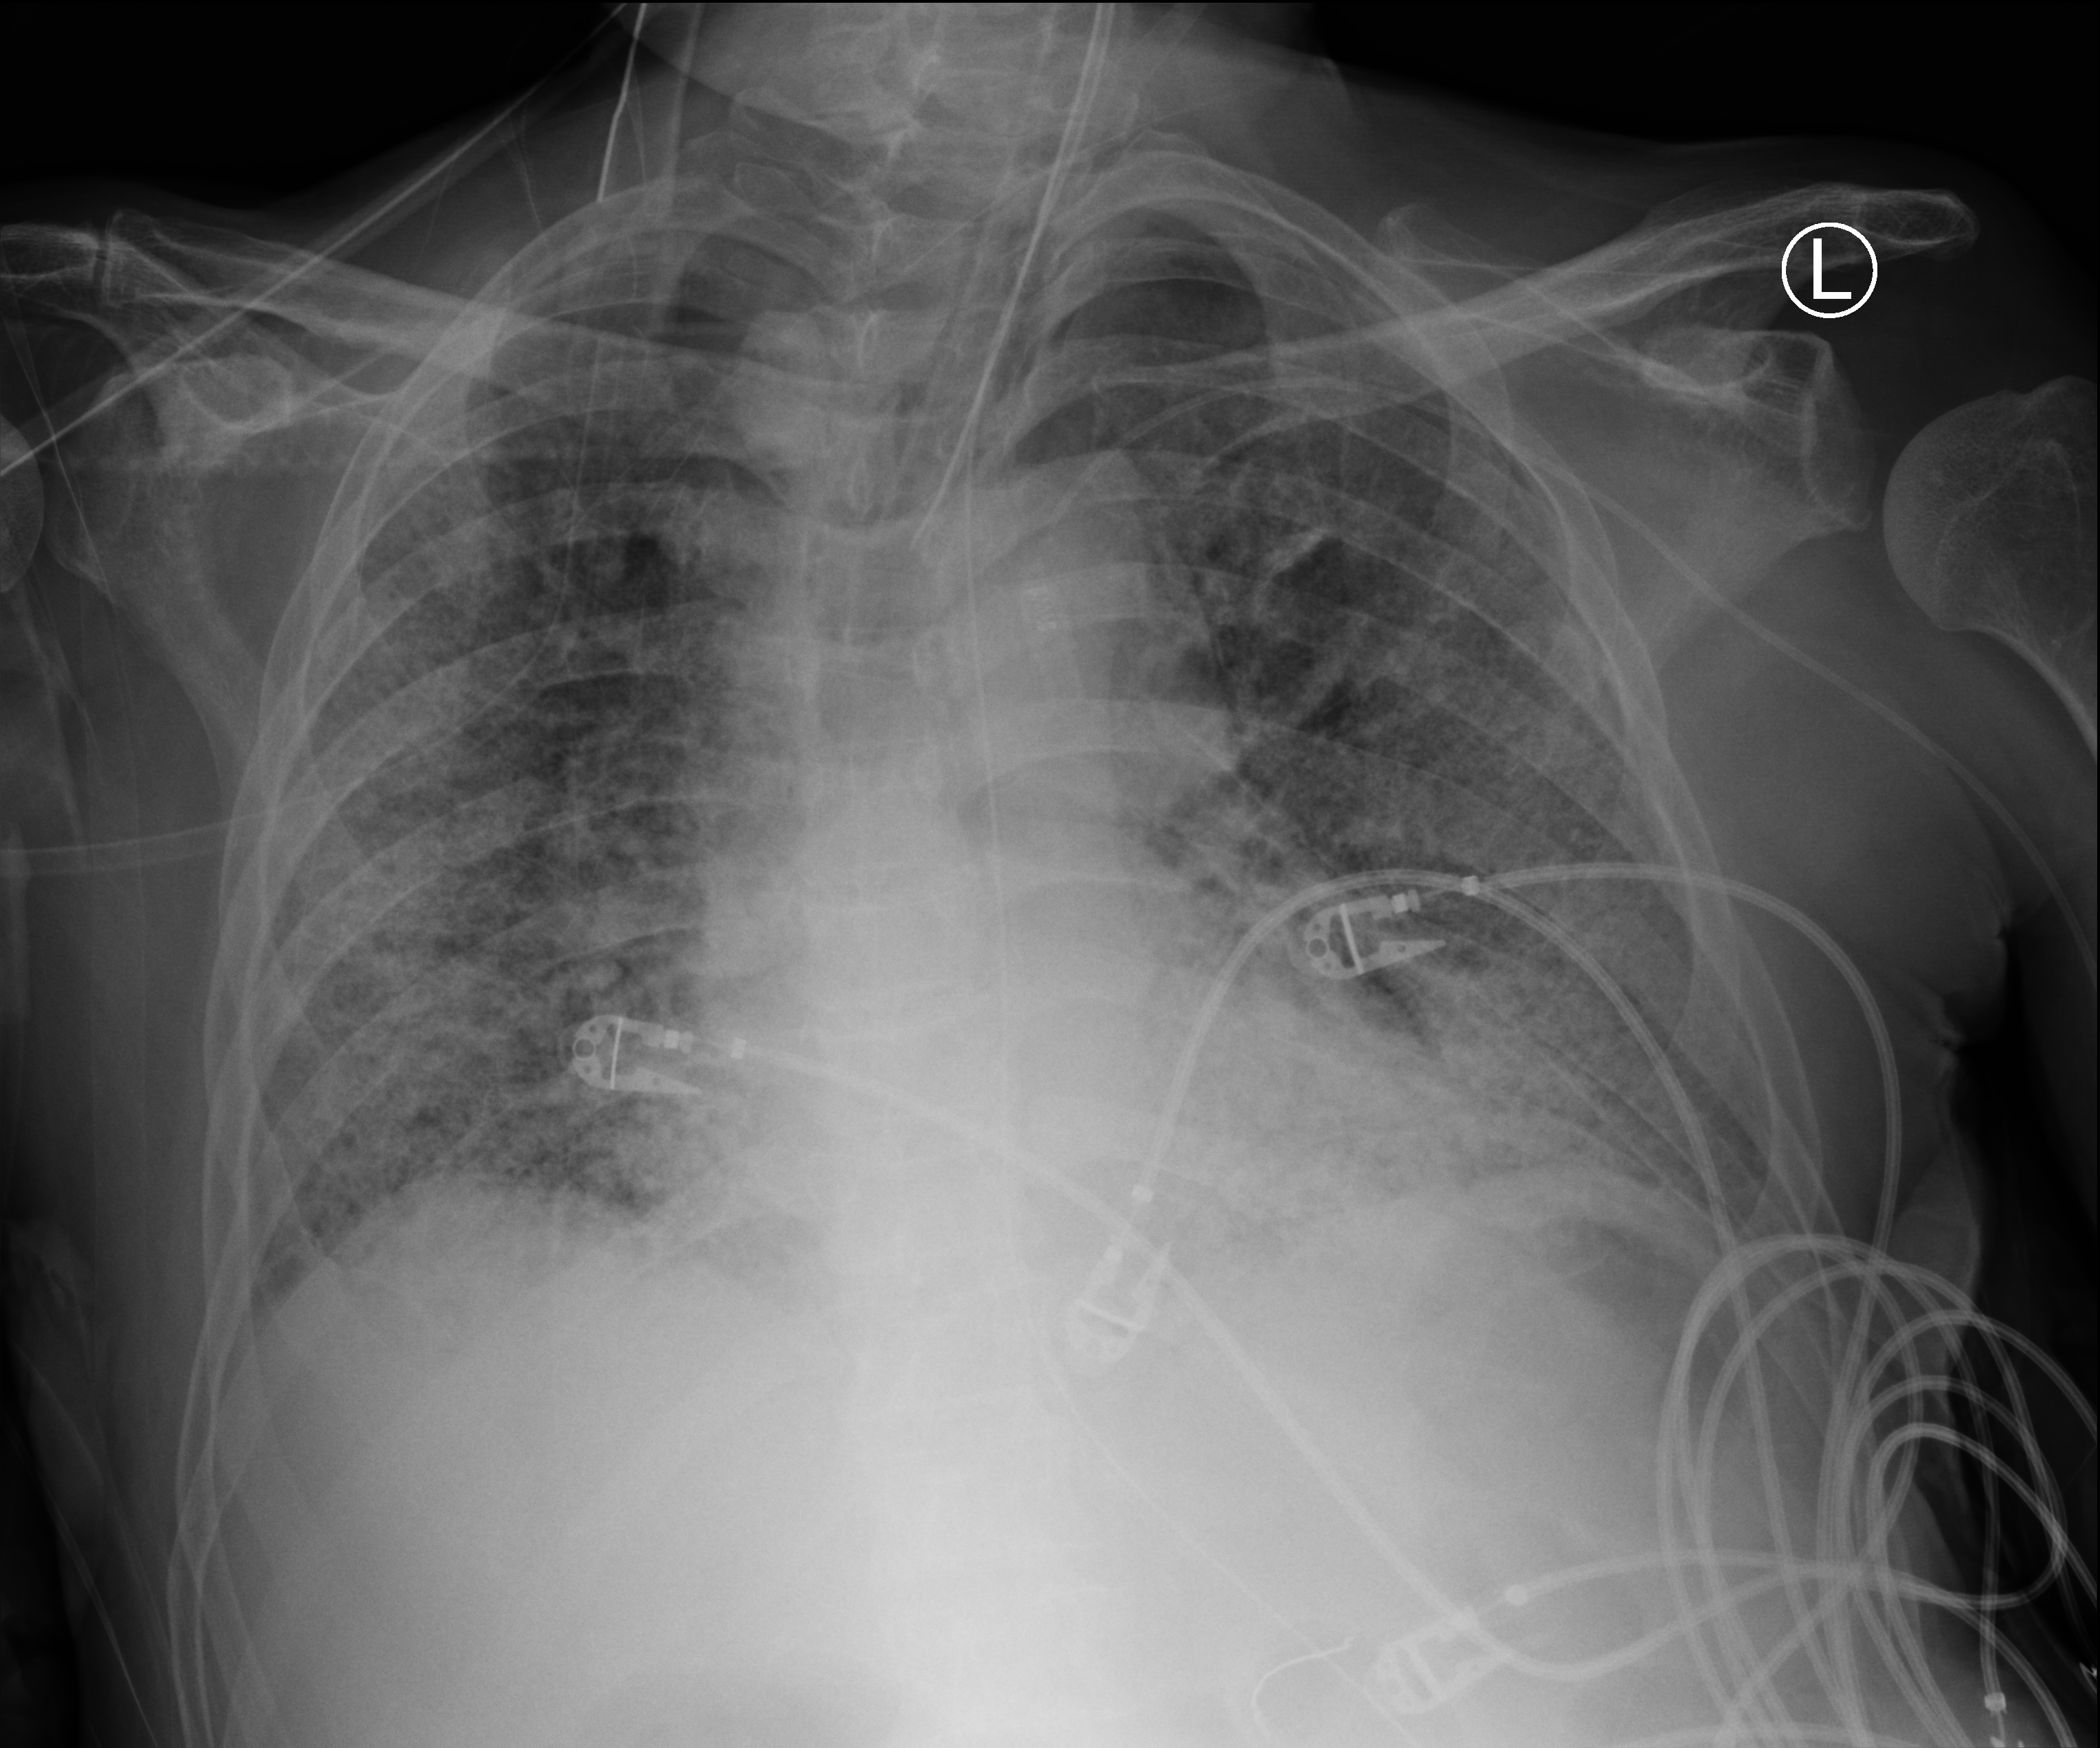
Portable chest radiograph, anteroposterior (AP) projection. Male patient hospitalised with COVID-19, age 60–74 years.
Hospital-stay facts (about this admission, not read from this image; timing relative to this image not recorded):
- length of hospital stay: 54 days
- admitted to intensive care during this hospital stay: yes